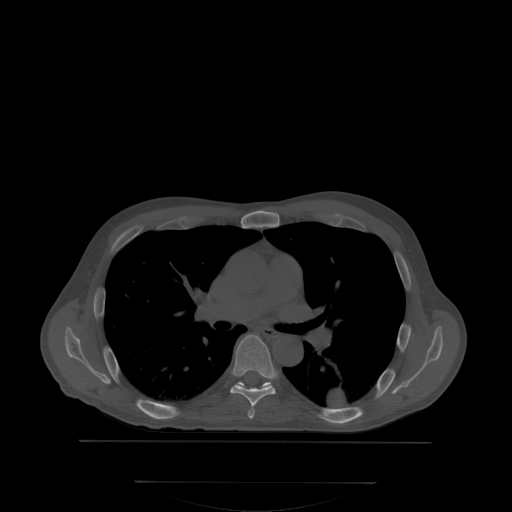
CT including the spine, one axial slice; position 236 of 350 along the scan axis; bone window (W 1800 / L 400 HU); 2.5 mm slice thickness; 512 × 512 image matrix, field of view 500 × 500 mm. Patient: male, 58 years. Case-level facts recorded for this patient, not image findings: primary cancer: prostate.
Structures marked on this image (semi-automatically segmented with operator editing):
- T6 vertebra: bounding box (x1, y1, x2, y2) in pixels: (231, 335, 277, 417)
- T7 vertebra: (236, 382, 274, 389)